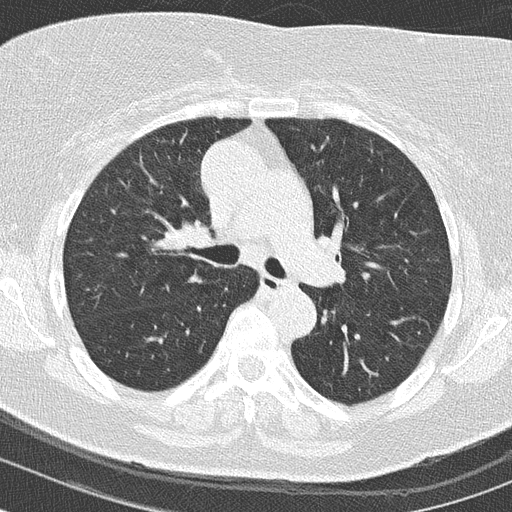
Axial slice from a low-dose chest CT screening exam; baseline annual screen; lung window (W 1500 / L -600 HU); 120 kVp; slice 51 of 149 in the series; 512 × 512 image matrix. Female participant, aged 63 years at enrolment. Former smoker at enrolment.
Lesion marked by an expert reader, bounding box [x1, y1, x2, y2] px = [150, 216, 224, 268]. No non-calcified nodule or mass ≥4 mm was recorded by the screening reader at this exam. Official screen result: negative screen, minor abnormalities not suspicious for lung cancer. Lung cancer was diagnosed 149 days after this screen: squamous cell carcinoma, keratinizing, NOS, right upper lobe, moderately differentiated (G2), stage IIA (AJCC 6th edition), 42 mm at pathology.